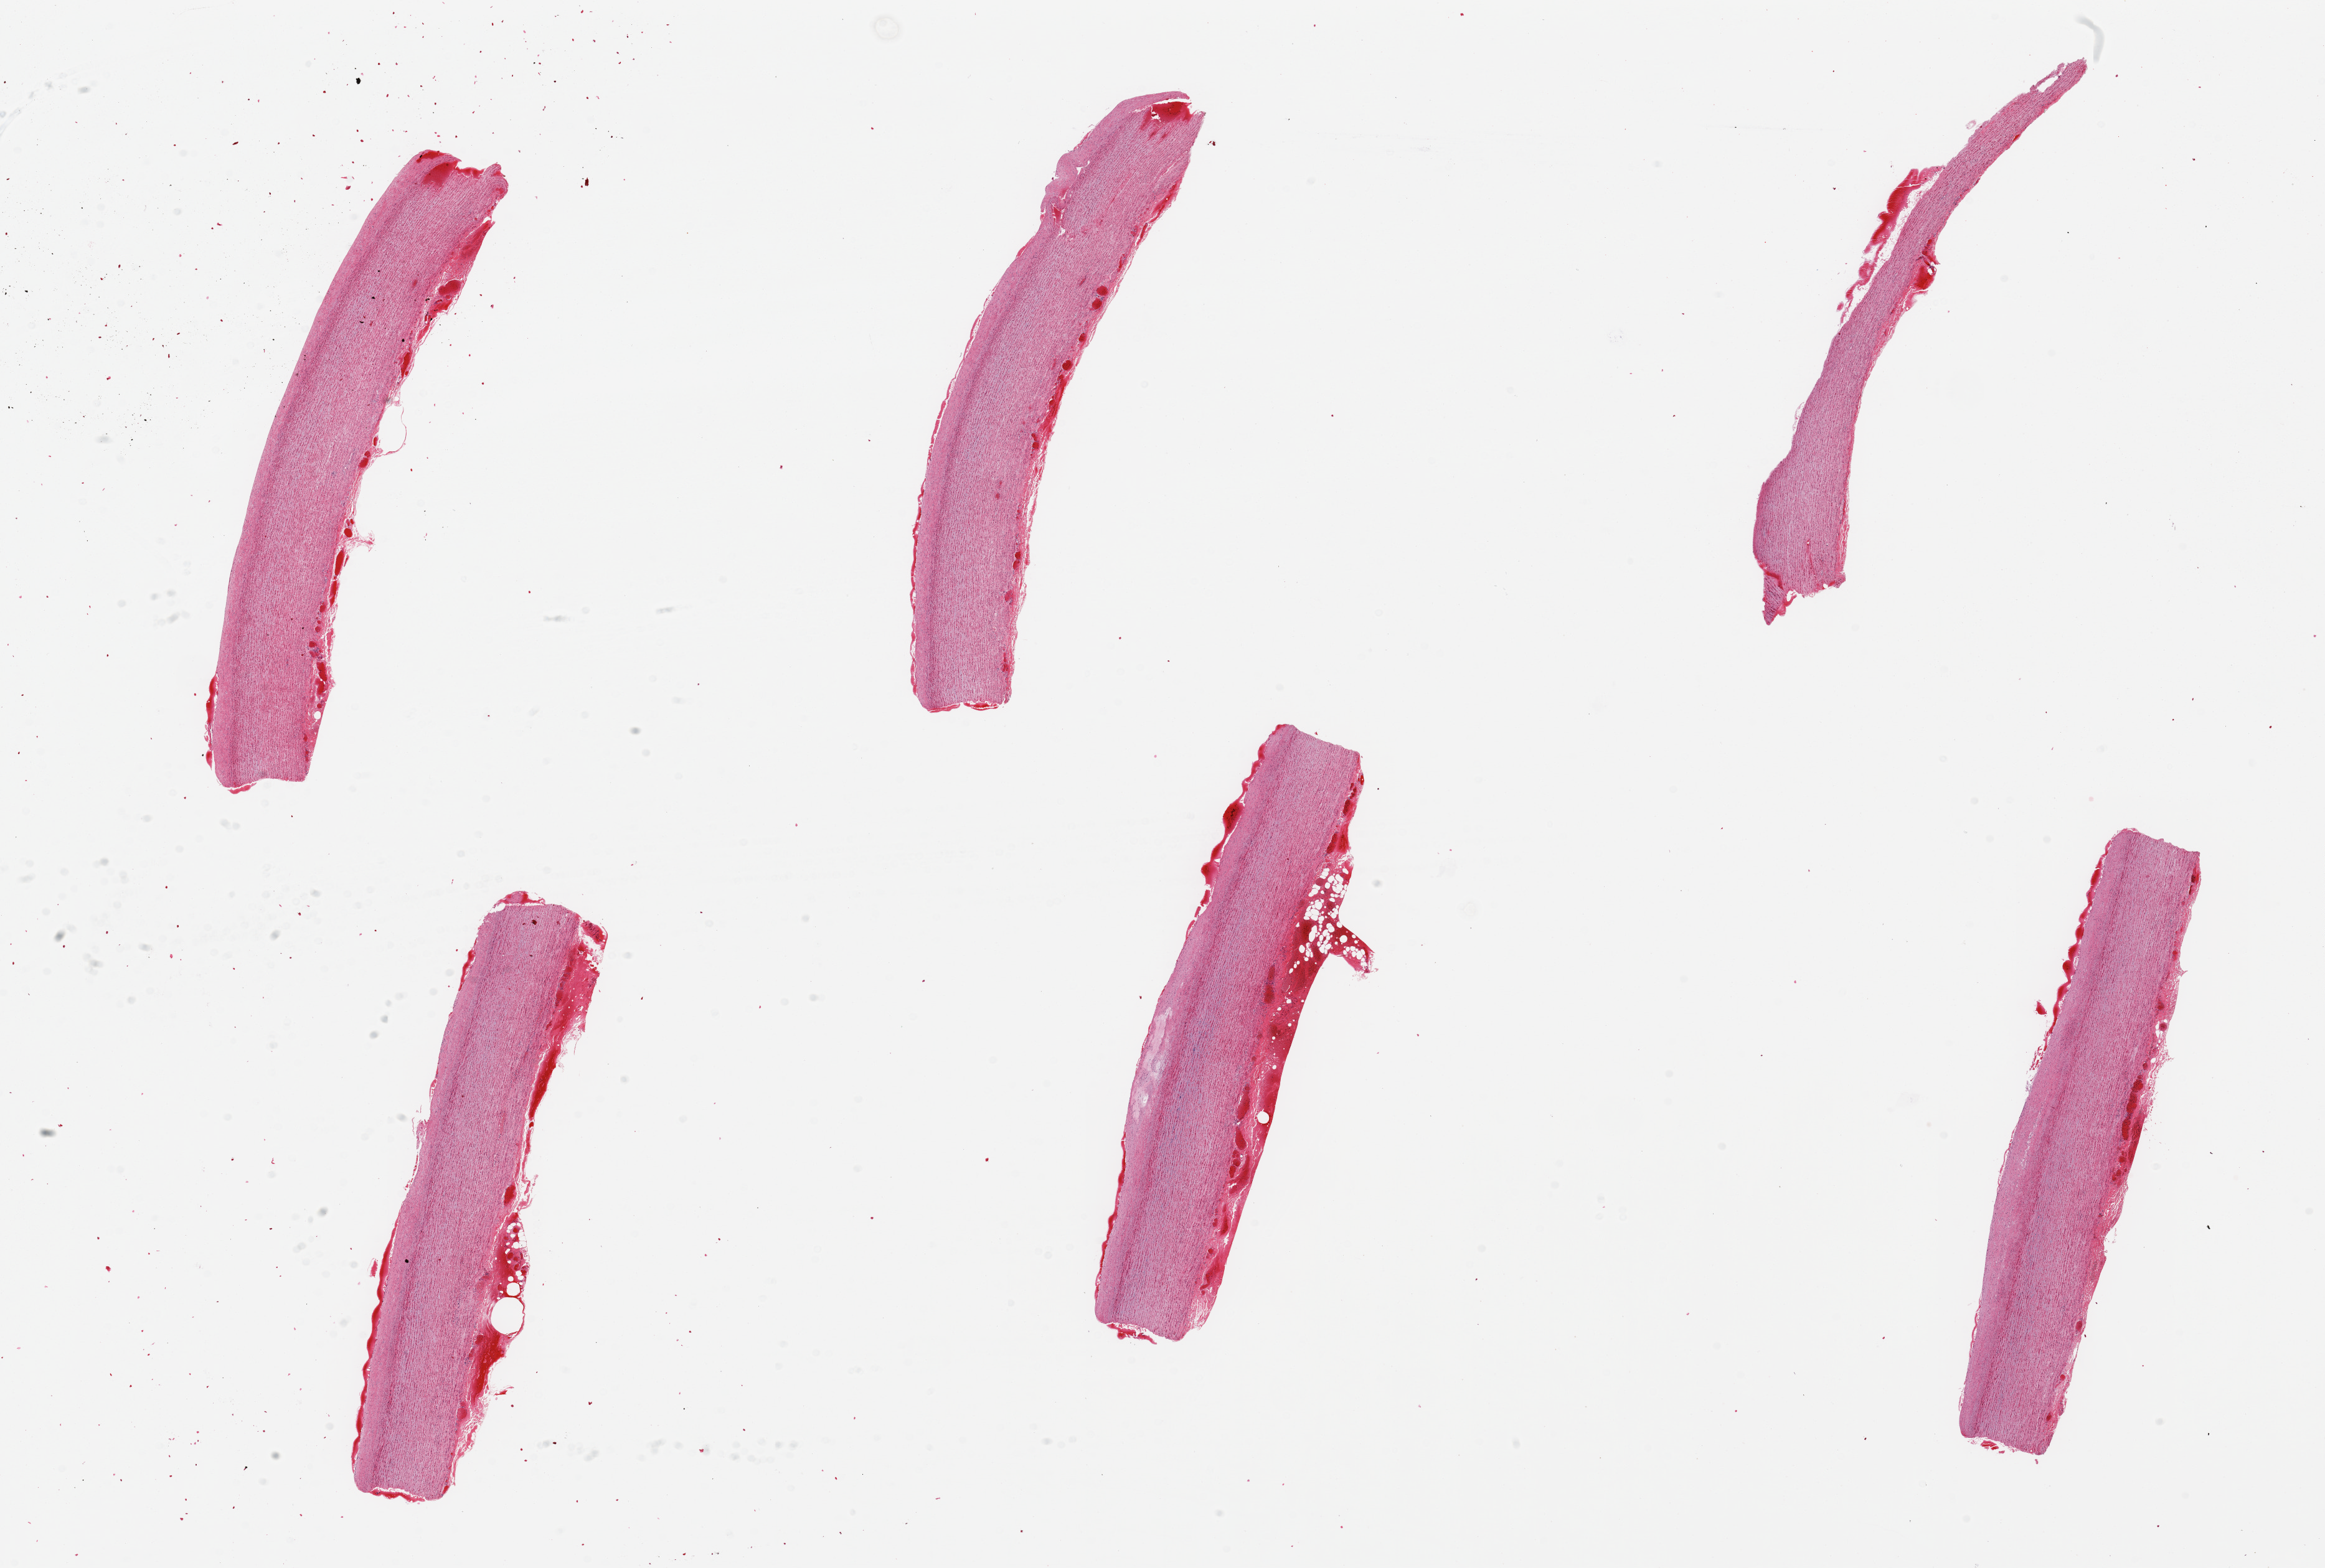
H&E whole-slide image, brightfield — a low-resolution overview of the entire scanned area, about 29.5 x 19.9 mm (acquisition: 20x scan). PAXgene-fixed paraffin-embedded (PFPE) section. Section of aorta (target tissue). Donor tissue sample. Donor: male.
Reviewer comment on this tissue sample: 6 pieces `8x1.5mm.